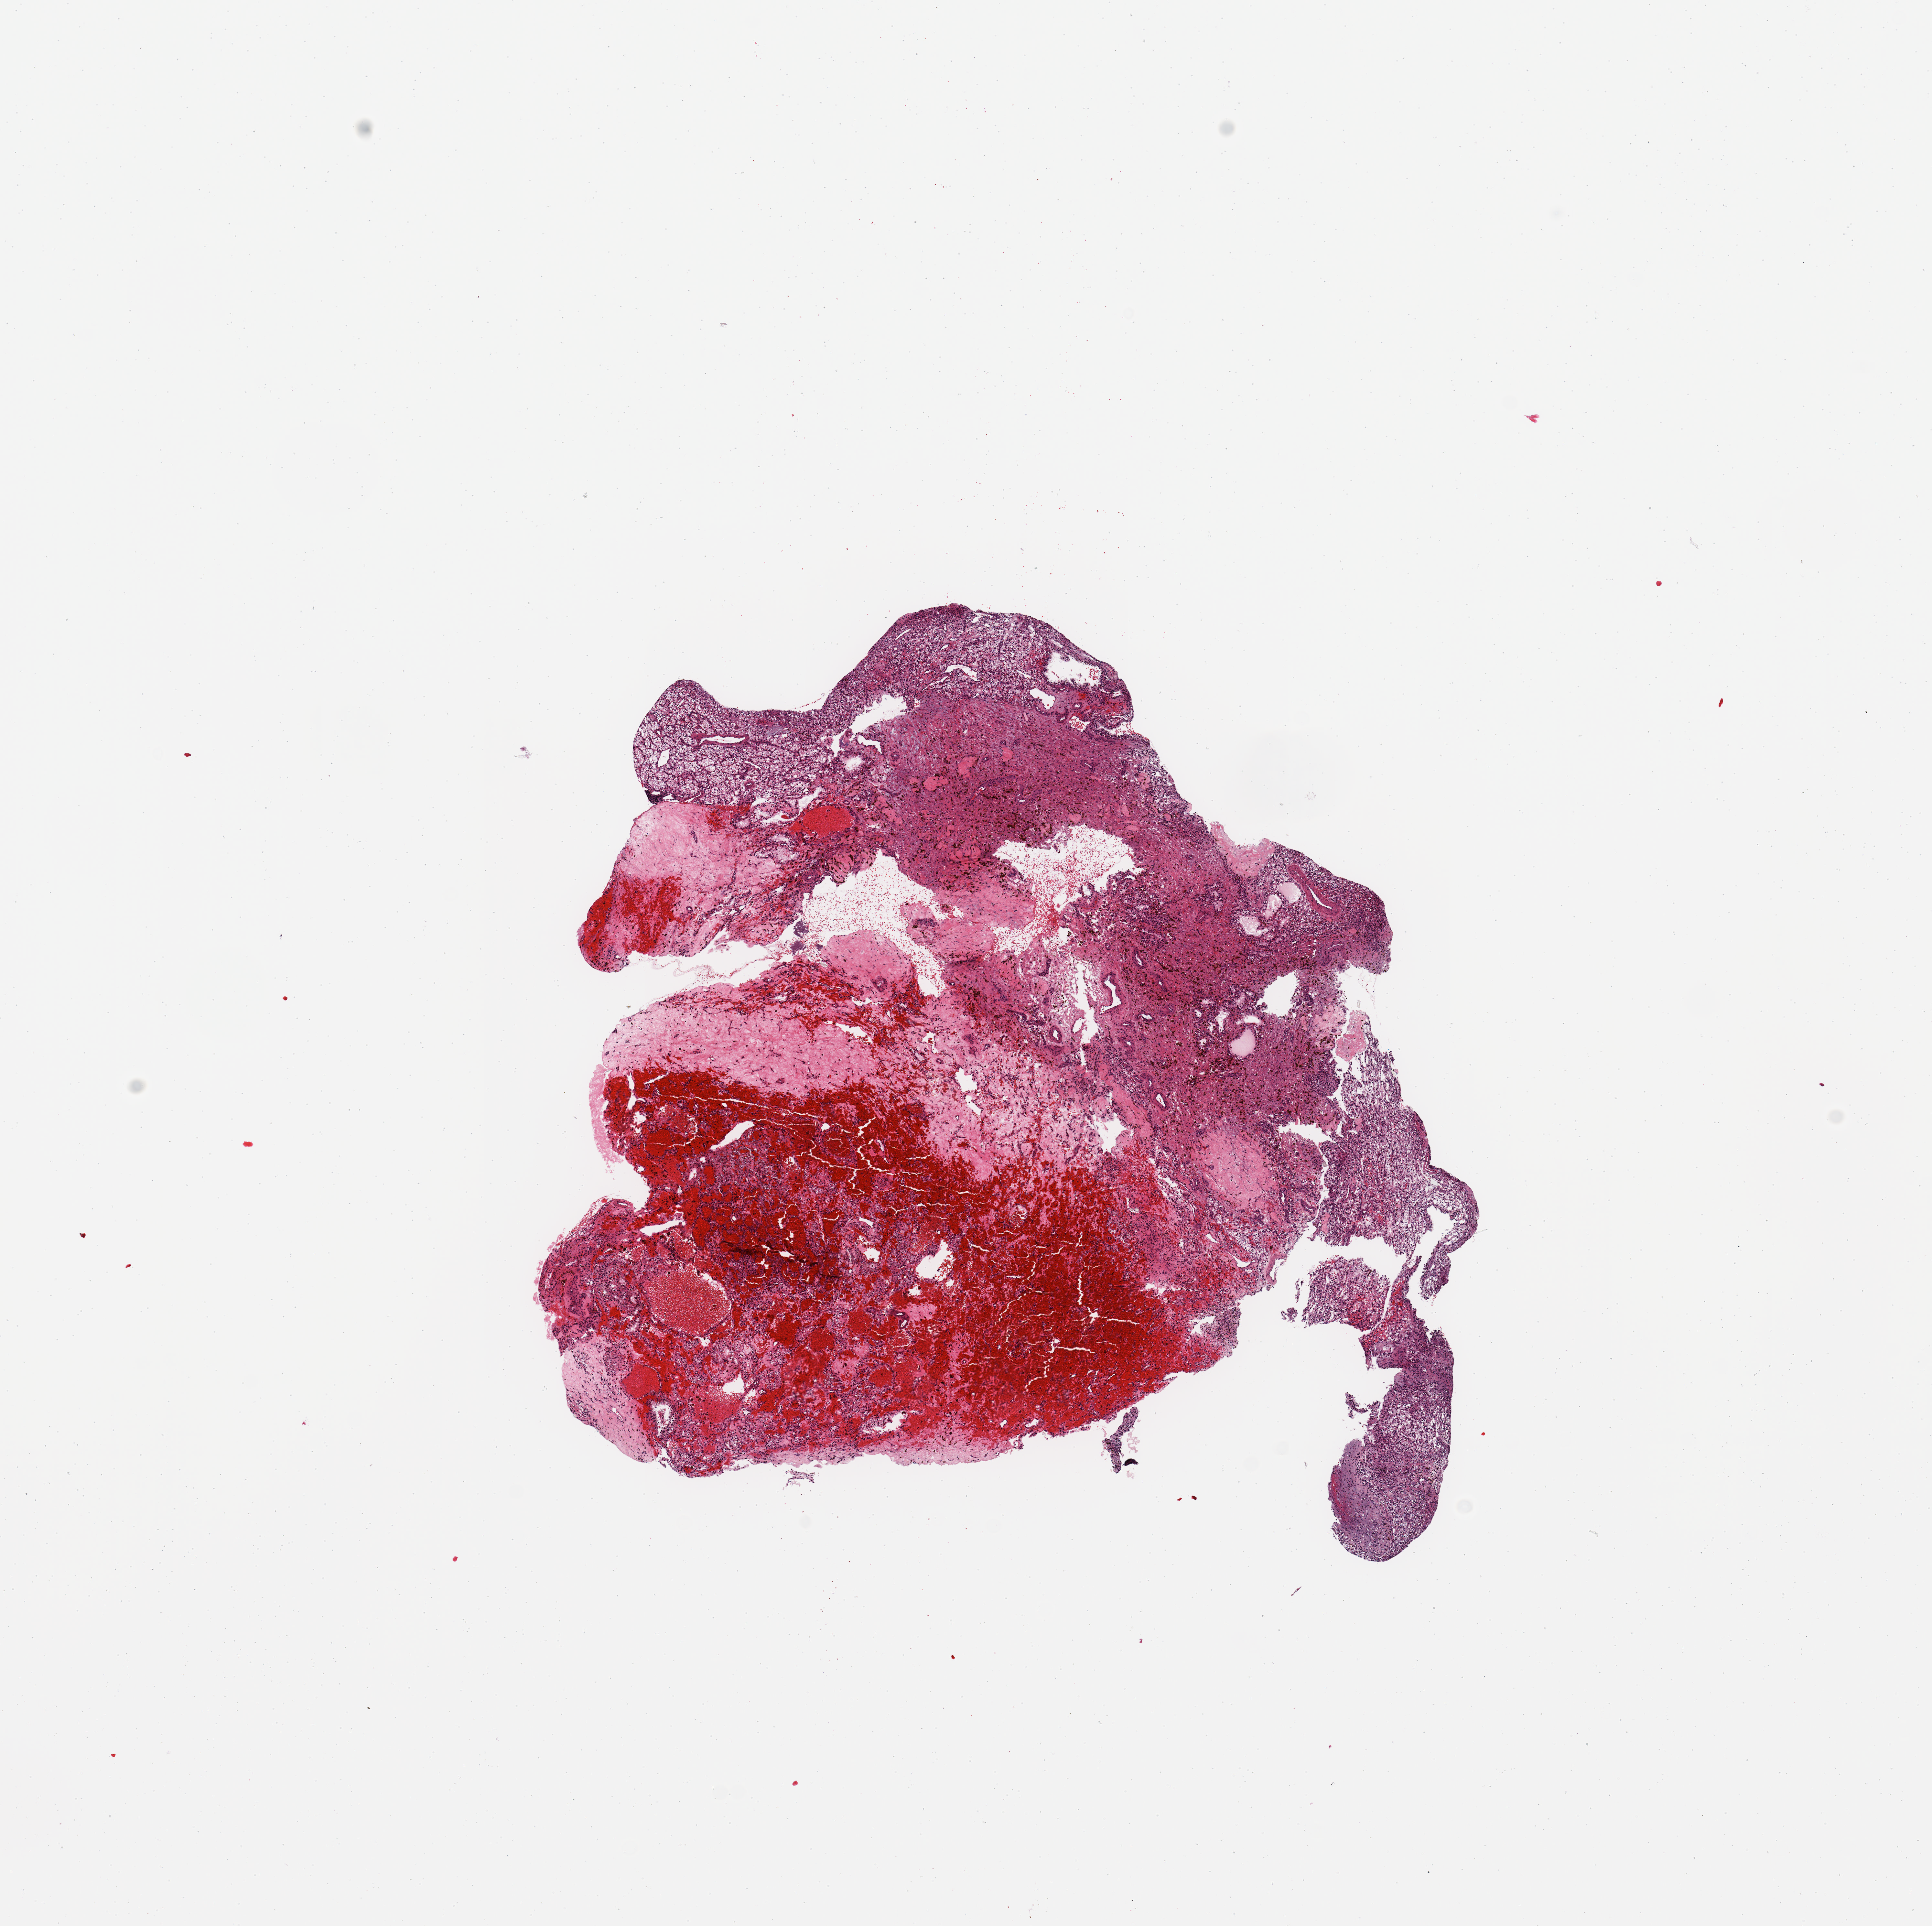
Whole-slide histology image, Hematoxylin and eosin (H&E) stained — shown as a low-resolution overview of the whole scanned area (about 11.8 x 11.8 mm), tumour tissue sample, kidney. Patient: male, age 67 years. Histologic grade: G2 (moderately differentiated).
* AJCC pathologic stage: I
* primary tumour site (as recorded): lower pole
* diagnosis: Renal cell carcinoma, NOS